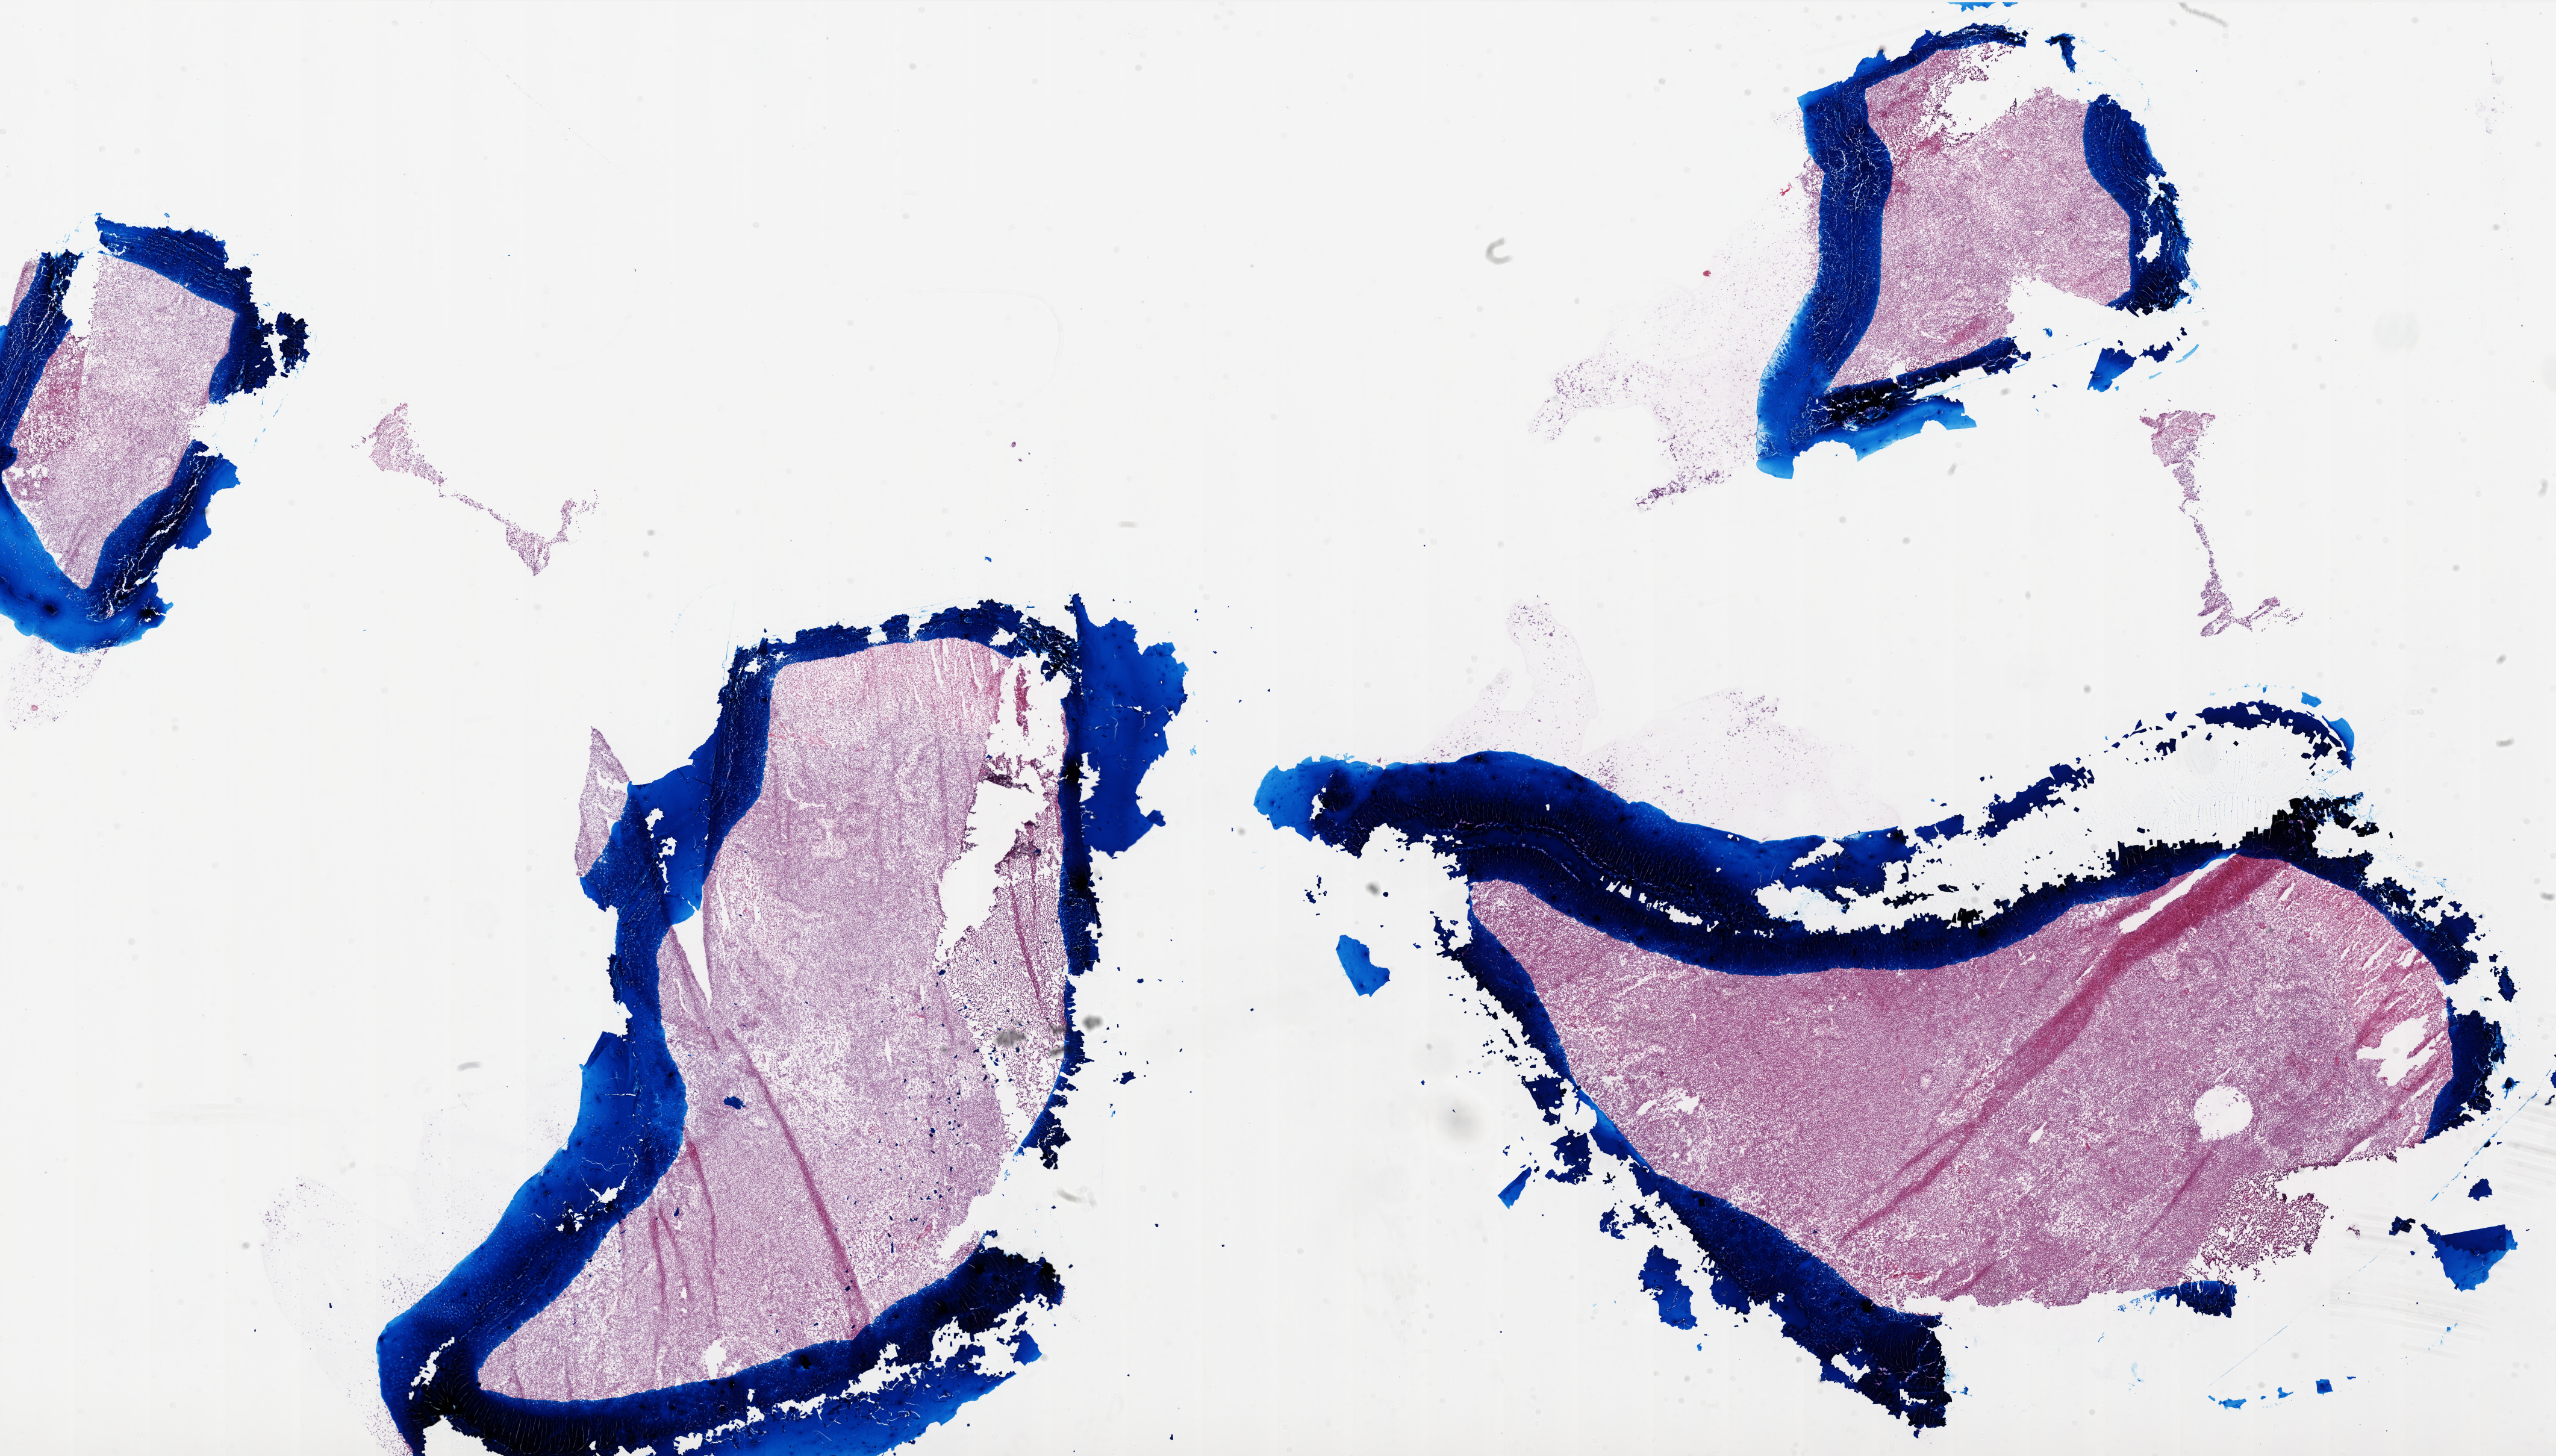
H&E whole-slide image, a low-resolution overview of the entire scanned area, about 34.0 x 19.4 mm (acquisition: 20x scan); frozen section from the top of the tissue portion; primary tumour sample from the brain. Male, age 39 years at initial diagnosis.
Histologic diagnosis: Glioblastoma.